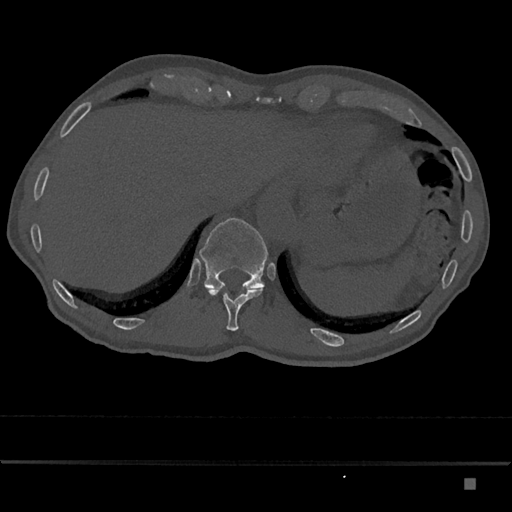
CT including the spine, one axial slice. Reconstruction kernel Br40s/3. Bone window (W 1800 / L 400 HU). 0.5 mm slice thickness. 512 × 512 image matrix, field of view 390 × 390 mm. Patient: male, 72 years. From the clinical record (not read from this slice): primary cancer: prostate.
Structures marked on this image (semi-automatically segmented with operator editing):
- T11 vertebra: bounding box <208,287,263,331> (left, top, right, bottom; pixels)
- T12 vertebra: <199,218,268,289>